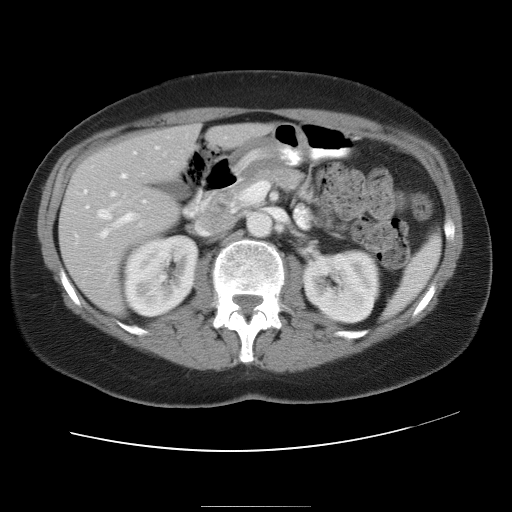
Contrast-enhanced abdominal CT, one axial slice. Reconstruction kernel STANDARD. 120 kVp. Intravenous contrast given. Soft-tissue window (W 400 / L 40 HU). 7.5 mm slice thickness. 512 × 512 image matrix. Female patient, age 52 years. From the clinical record (not read from this slice): diagnosis: colorectal cancer liver metastases, imaged before liver resection; multiple liver metastases: no; largest metastasis: 3 cm; disease in both lobes: yes.
Outlined on this slice (manually delineated by an expert):
- hepatic veins: bounding box [x1, y1, x2, y2] px = [98, 154, 165, 219]
- liver: [59, 123, 269, 312]
- planned liver remnant (the part of the liver to remain after resection): [161, 123, 270, 163]
- portal vein (with intrahepatic branches): [101, 174, 145, 238]